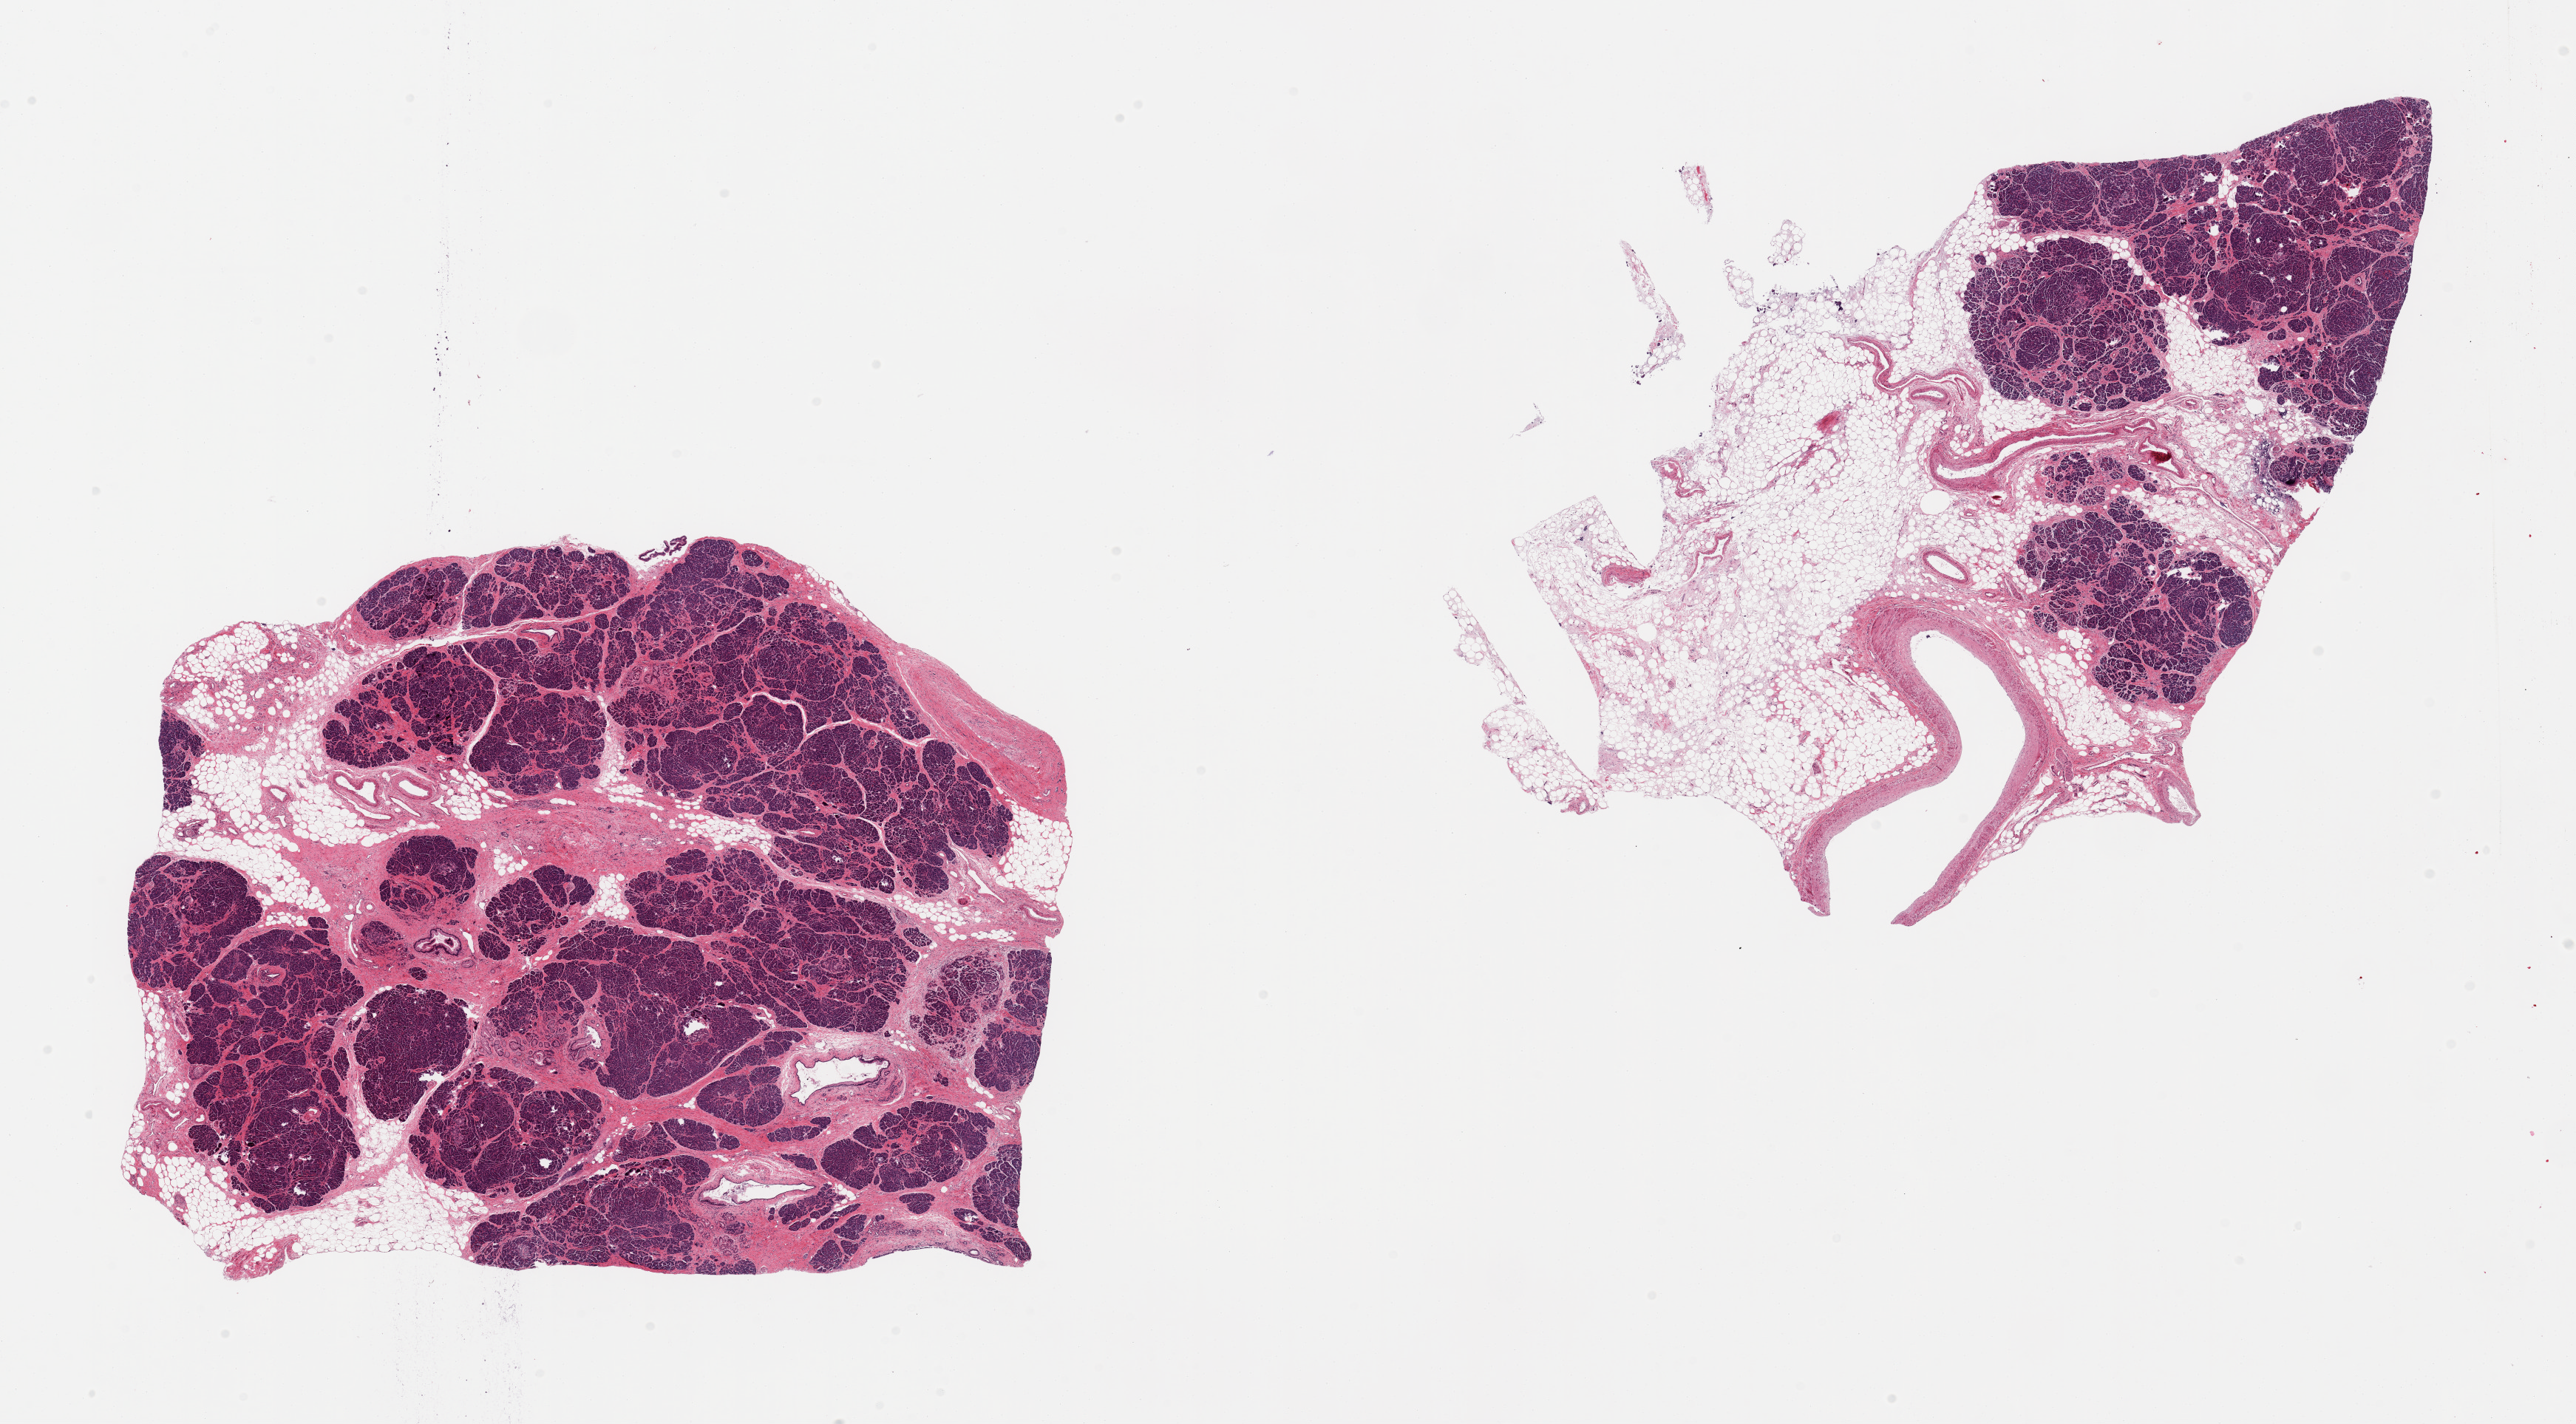
Whole-slide image, haematoxylin and eosin stain — a low-resolution overview of the entire scanned area, about 27.6 x 15.2 mm (from a 20x scan); PAXgene-fixed paraffin-embedded (PFPE) section; target tissue: pancreas; tissue donor sample. Donor sex: male.
- review note (as recorded): 2 pieces; one is 60% attached fat and vessels, second is ~20% fat, fibrosis, PanIN IA